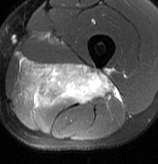
MRI of an extremity soft-tissue mass, one axial slice. Position 39 of 70 along the scan axis. T2-weighted fat-saturated. MR volume resampled by the dataset authors to the PET/CT grid (not the native acquisition matrix). 3.27 mm slice thickness. 158 × 164 image matrix, field of view 154 × 160 mm. Male patient. From the clinical record (not read from this slice): histological type: extraskeletal osteosarcoma; grade: high; site of the primary tumour: left adductur.
Annotated regions visible in this slice (expert contour drawn on MRI and transferred to this co-registered scan by the dataset authors):
- gross tumour volume (mass): bounding box [x1, y1, x2, y2] px = [13, 59, 121, 108]